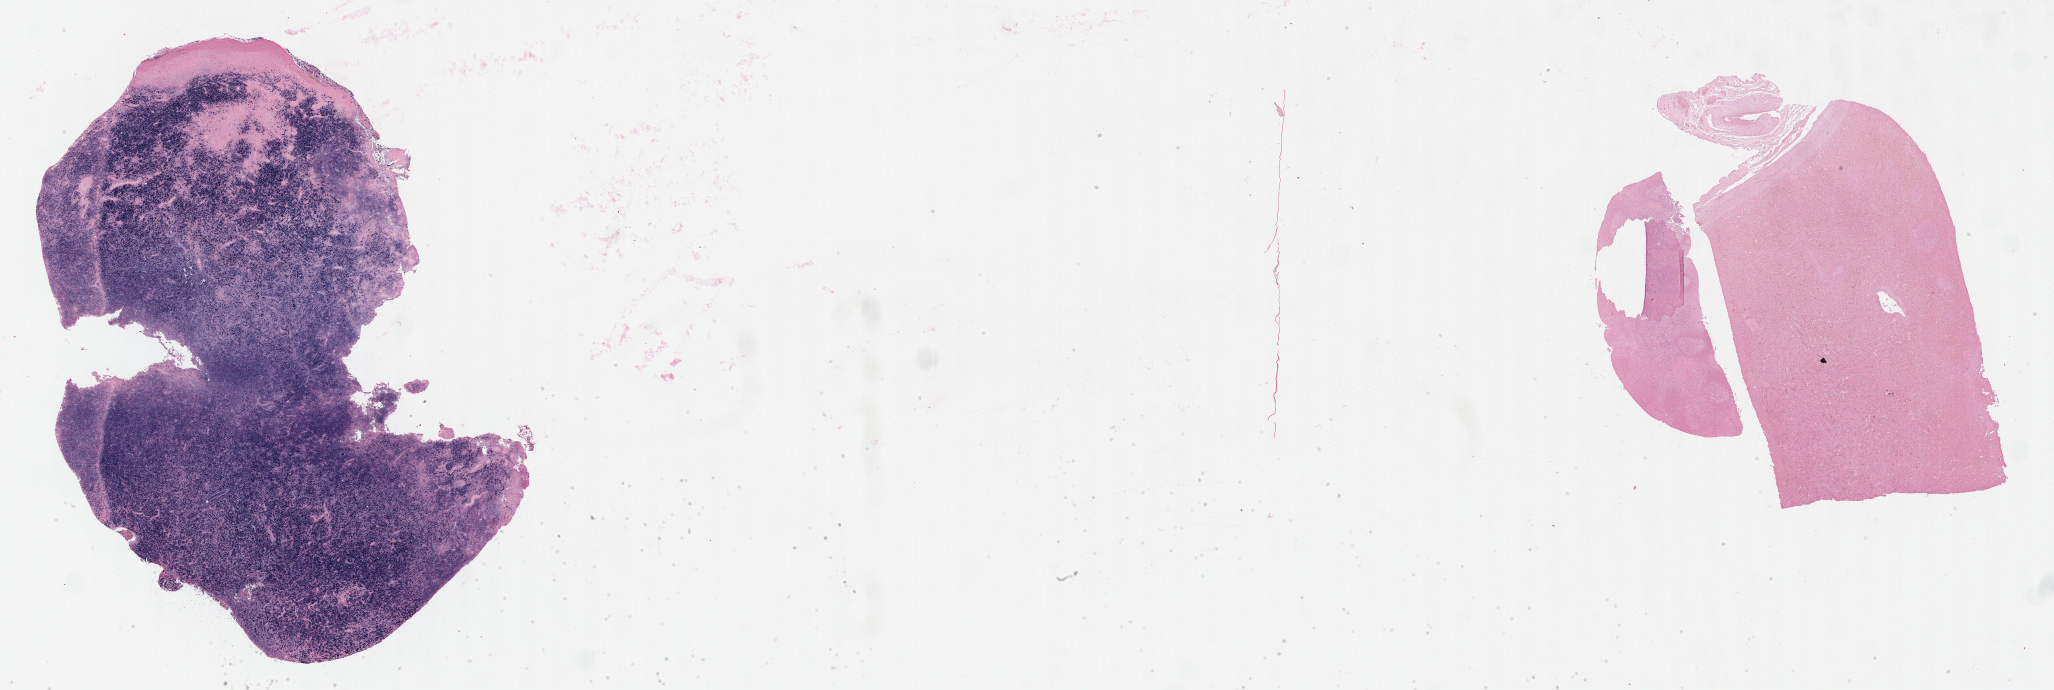
Whole-slide image, Epstein–Barr virus-encoded RNA (EBER) in-situ hybridisation, shown as a low-resolution overview of the whole scanned area (about 33.2 x 11.2 mm), tumor tissue. Male patient; age at initial diagnosis 7 years.
Histologic diagnosis: Diffuse large B-cell lymphoma, NOS.